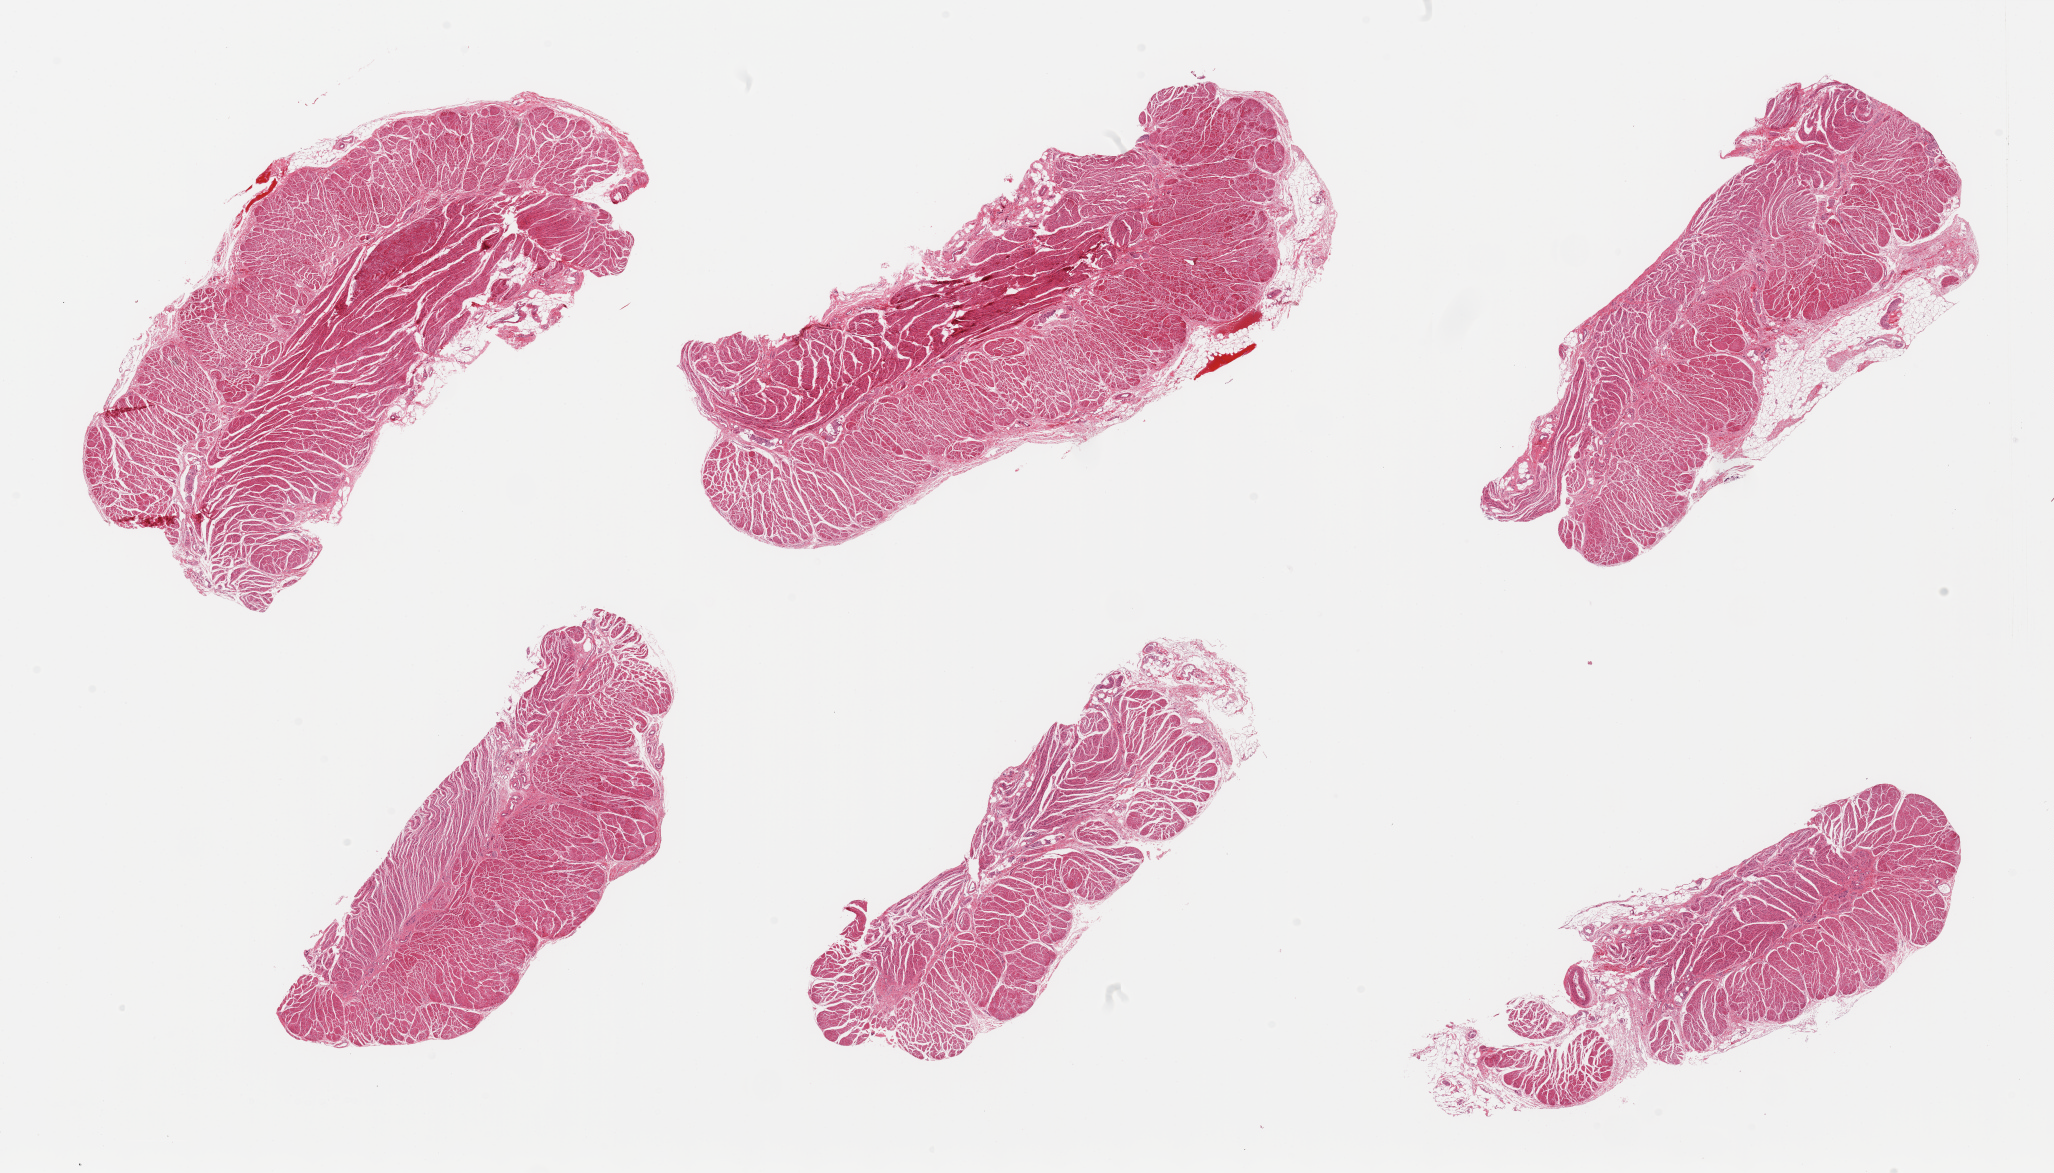
Haematoxylin and eosin whole-slide image — whole scanned area (about 32.5 x 18.6 mm) shown as a low-resolution overview. PAXgene-fixed, paraffin-embedded tissue. Sampled site (target tissue): gastroesophageal junction. Tissue donor sample. Male donor.
Review note (as recorded): 6 pieces.